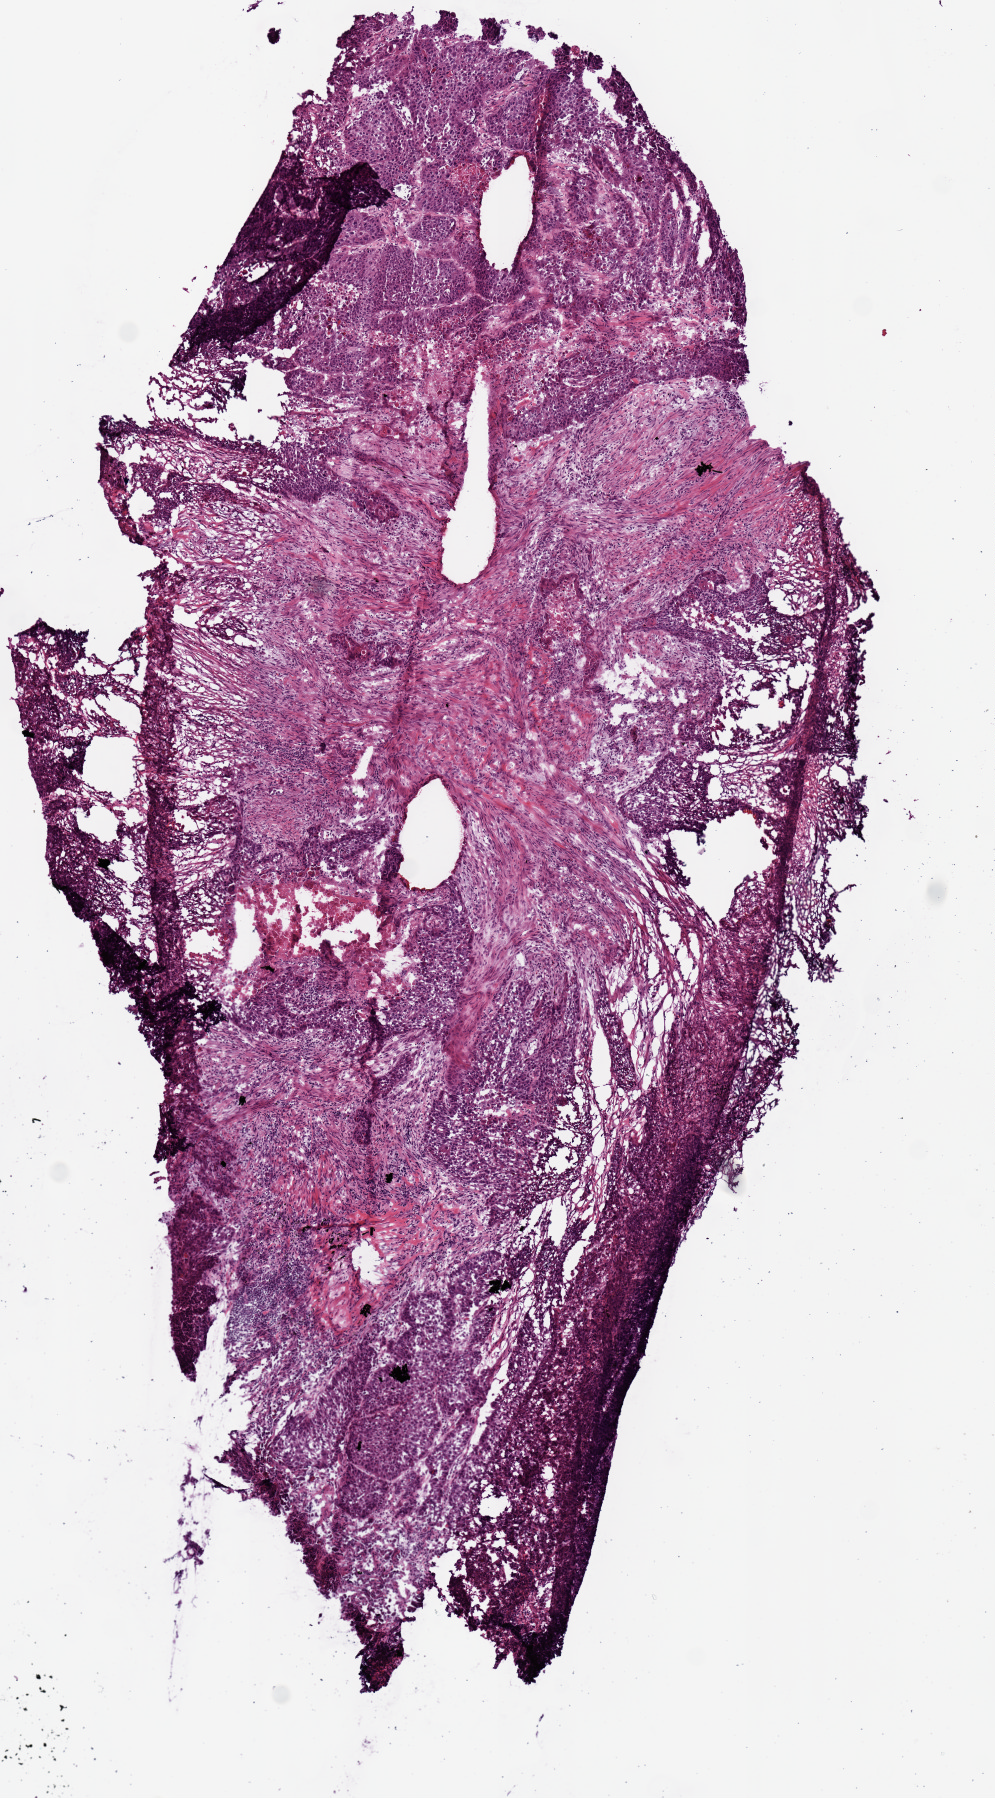
Digitized H&E tissue section (whole slide), shown as a low-resolution overview of the whole scanned area (about 3.9 x 7.1 mm). Frozen section from the top of the tissue portion. Sample: primary tumour, lung. Patient: male, age at initial diagnosis 67 years. Slide review estimates, as recorded: tumour cells 85%, tumour nuclei 75%, normal cells 0%, stromal cells 15%, necrosis 0%.
Diagnosis: Squamous cell carcinoma, NOS (lower lobe, lung). TNM: T1 N0 M0. AJCC pathologic stage: IA (6th edition).